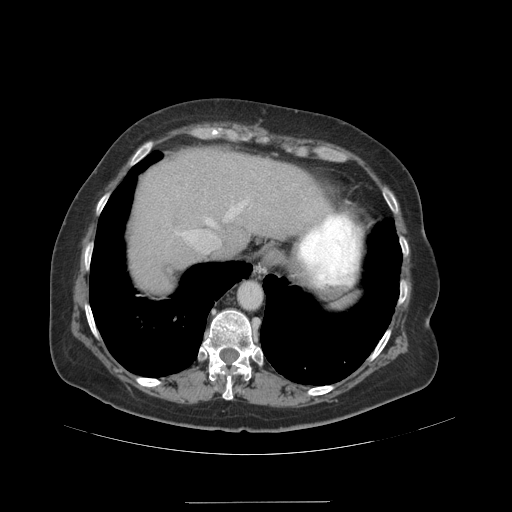
Contrast-enhanced abdominal CT (liver protocol), one axial slice. Position 81 of 99 along the scan axis. 140 kVp. Soft-tissue window (W 400 / L 40 HU). 2.5 mm slice thickness. 512 × 512 image matrix, field of view 440 × 440 mm. Case-level facts recorded for this patient, not image findings: diagnosis: hepatocellular carcinoma (patient treated with transarterial chemoembolisation; whether this scan precedes or follows treatment is not stated here); TNM stage (as recorded): Stage-IVA; Child-Pugh class: A; tumour nodularity: multinodular.
Annotated regions visible in this slice (semi-automatically segmented with operator editing):
- abdominal aorta: bounding box (x1, y1, x2, y2) in pixels: (239, 282, 261, 309)
- liver parenchyma outside the tumour (the mass and vessels are separate outlines, so this box may not span the whole liver): (130, 148, 330, 292)
- liver vessels: (176, 200, 248, 249)